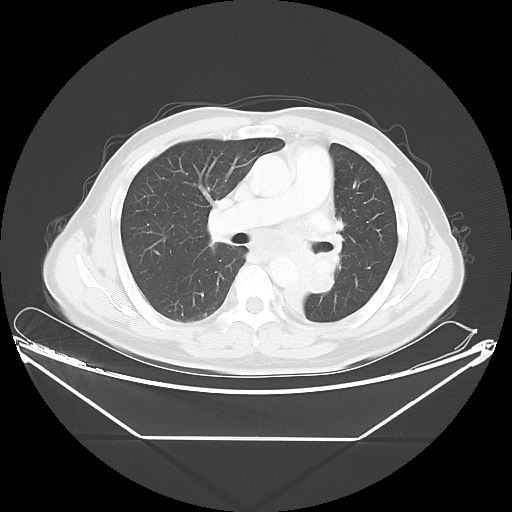
Chest CT, one axial slice; position 27 of 48 along the scan axis; 120 kVp; lung window (W 1500 / L -600 HU); 5 mm slice thickness; 512 × 512 image matrix, field of view 438 × 438 mm. Patient: male, 58 years. Case-level facts recorded for this patient, not image findings: clinical TNM (as recorded): T3 N3 M0.
Outlined on this slice (rectangle marked by the reading radiologist):
- lung tumour (recorded histology: squamous cell carcinoma): bounding box <270,234,349,335> (left, top, right, bottom; pixels)